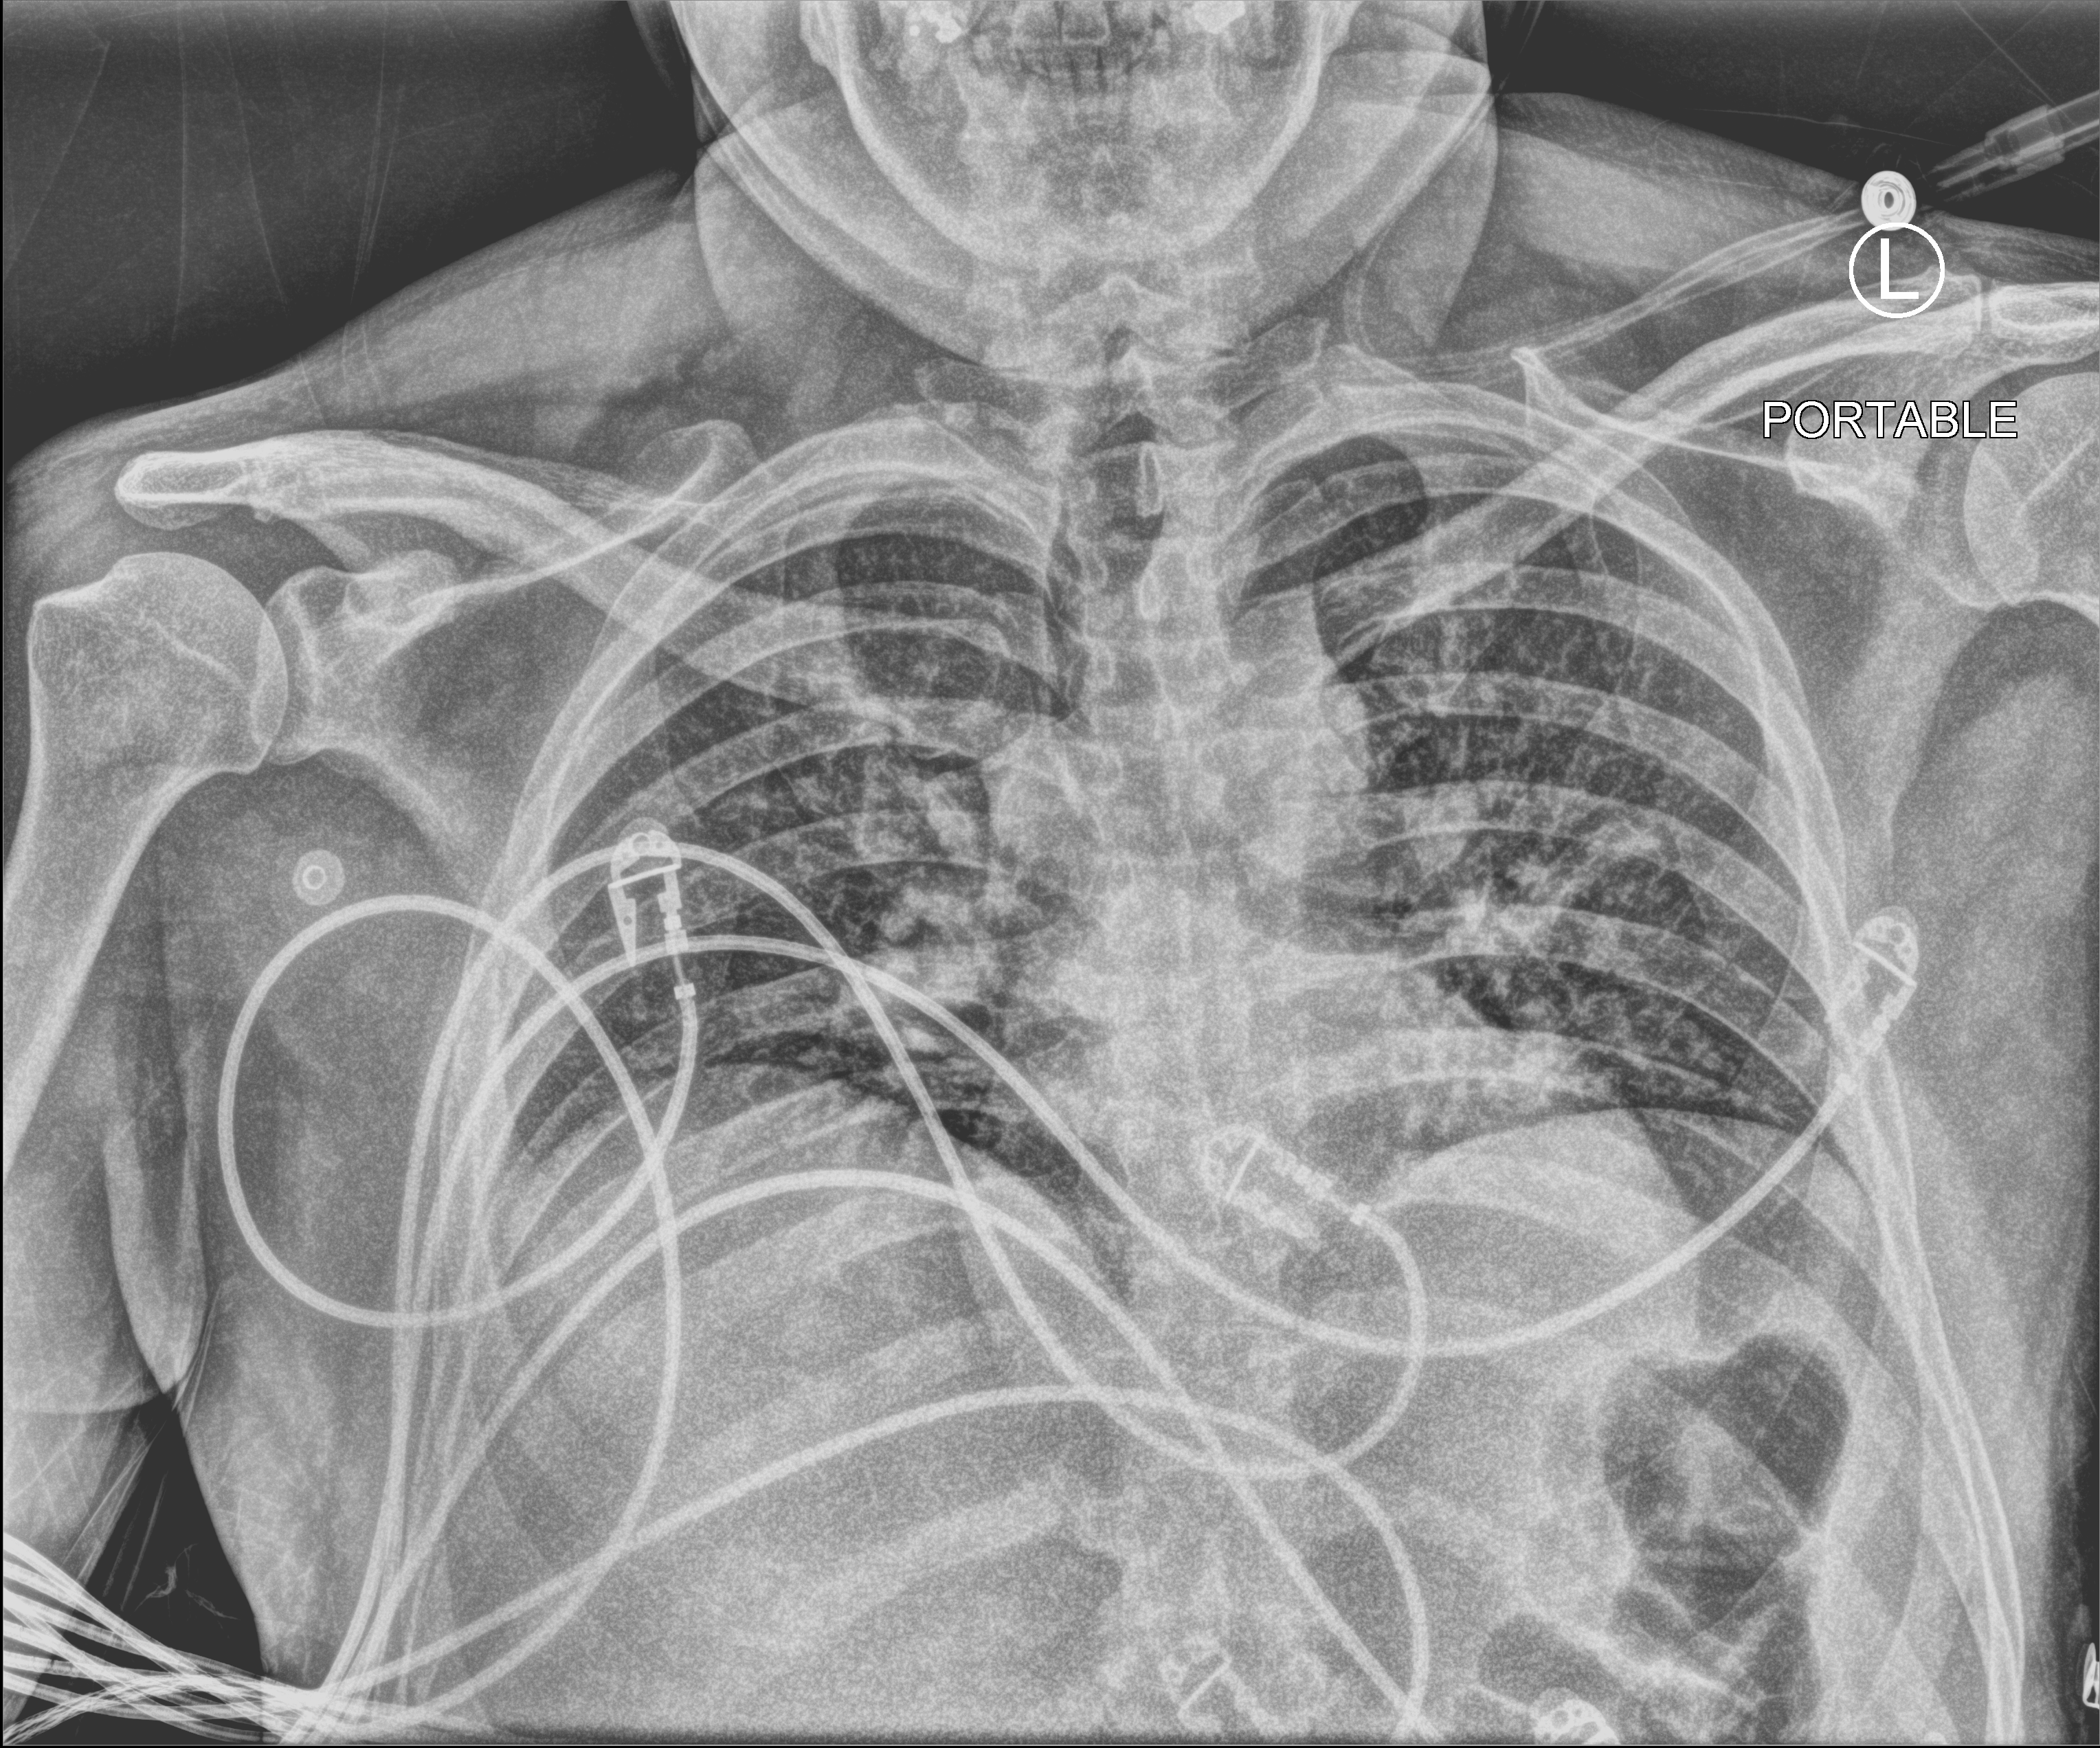
Portable chest radiograph, anteroposterior (AP) projection. Adult patient hospitalised with COVID-19, age 18–59 years.
Admission-level facts for this patient (not findings on this image; timing relative to this image not recorded):
- mechanically ventilated during this hospital stay: no